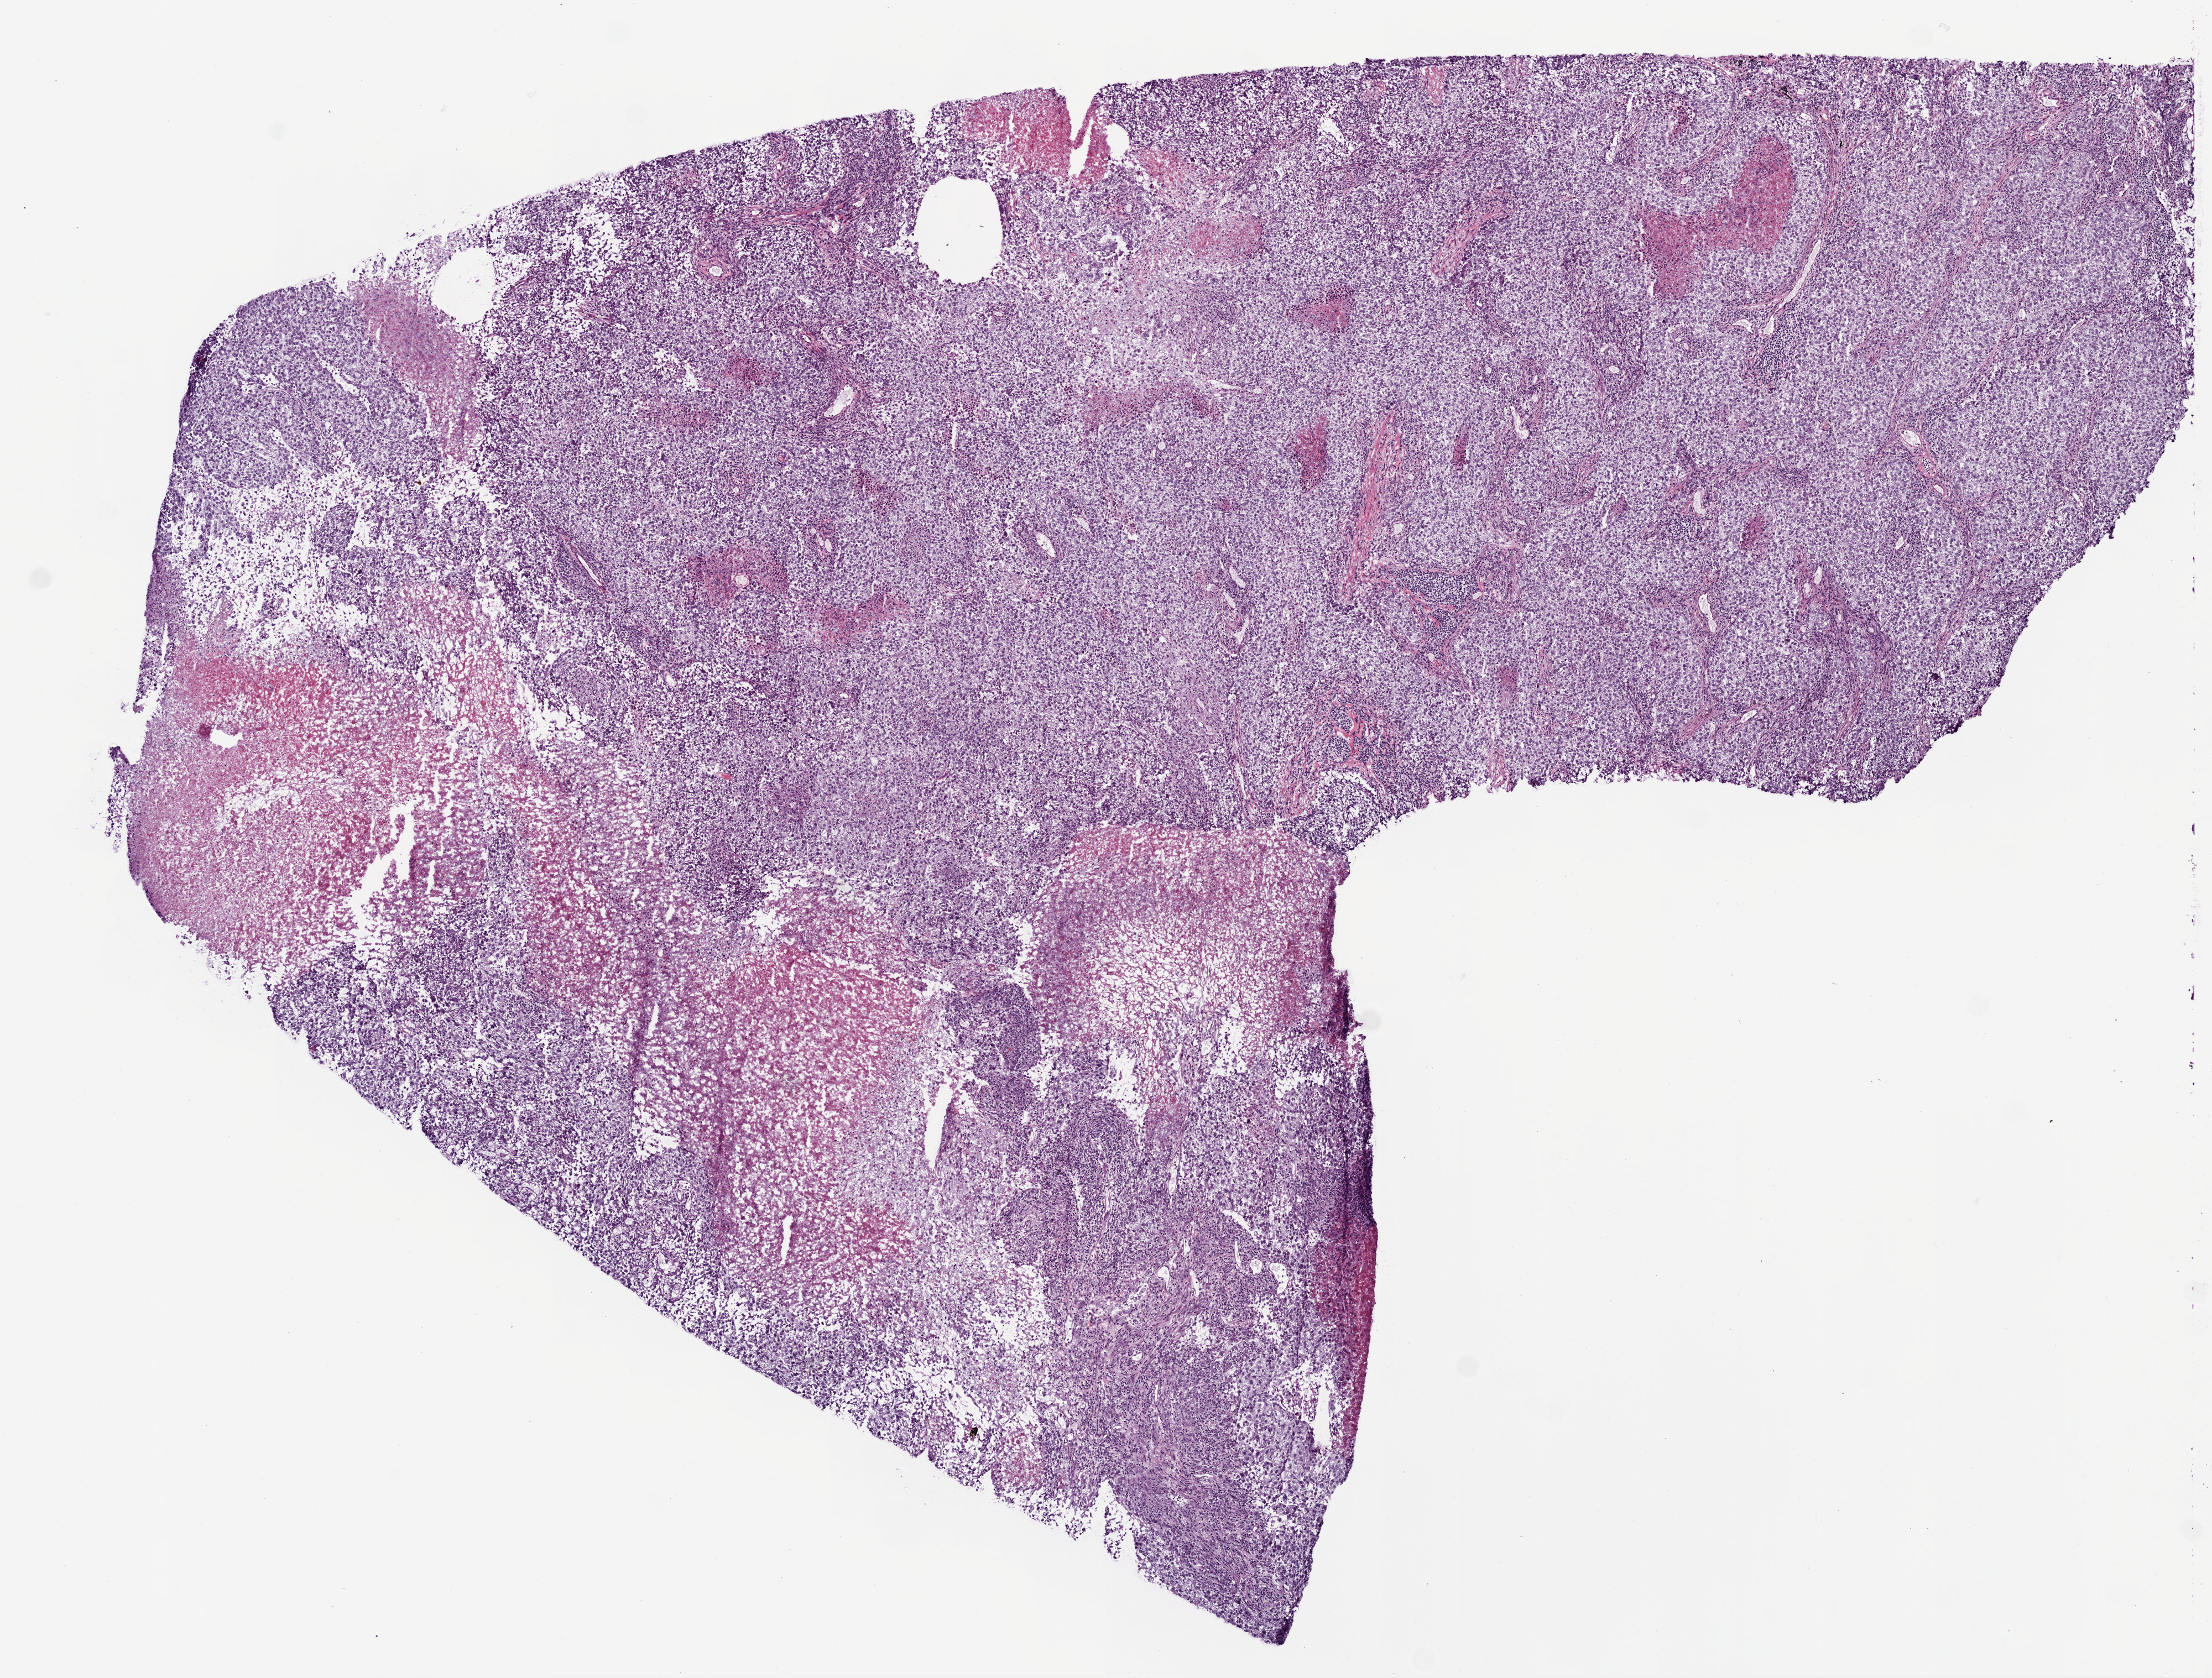
Digitized Hematoxylin and eosin (H&E) stained tissue section (whole slide) — shown as a low-resolution overview of the whole scanned area (about 8.0 x 6.1 mm, acquisition: 20x scan). Frozen section from the top of the tissue portion. Lung, primary tumour sample. Male patient.
Pathologic diagnosis: Solid carcinoma, NOS (upper lobe, lung).